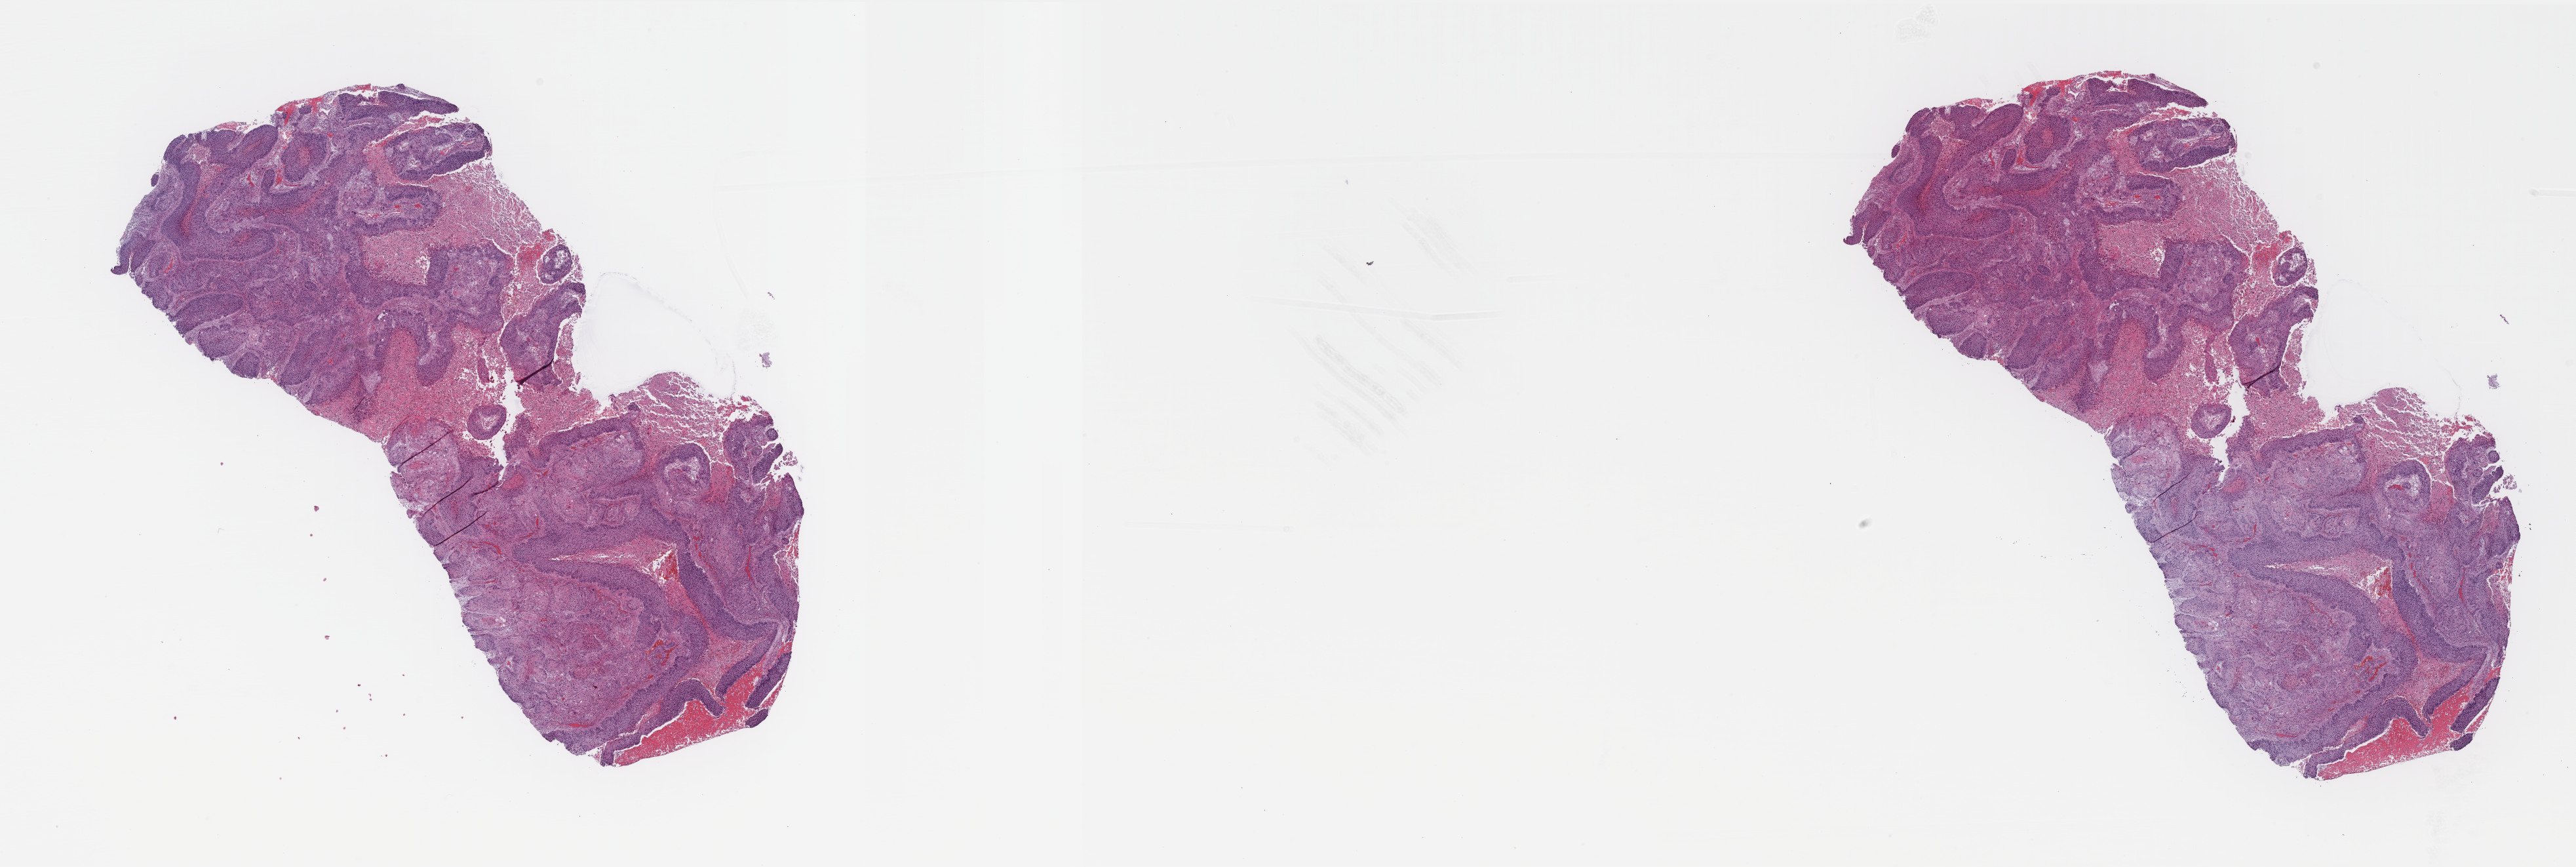
Digitized Hematoxylin and eosin (H&E) stained tissue section (whole slide) — low-resolution overview of the scanned area, about 31.5 x 10.6 mm. Formalin-fixed paraffin-embedded (FFPE) diagnostic section. Sample: primary tumour, lung. Patient: male, age at initial diagnosis 66 years.
• AJCC pathologic stage: IIA (7th edition)
• diagnosis: Squamous cell carcinoma, NOS (upper lobe, lung)